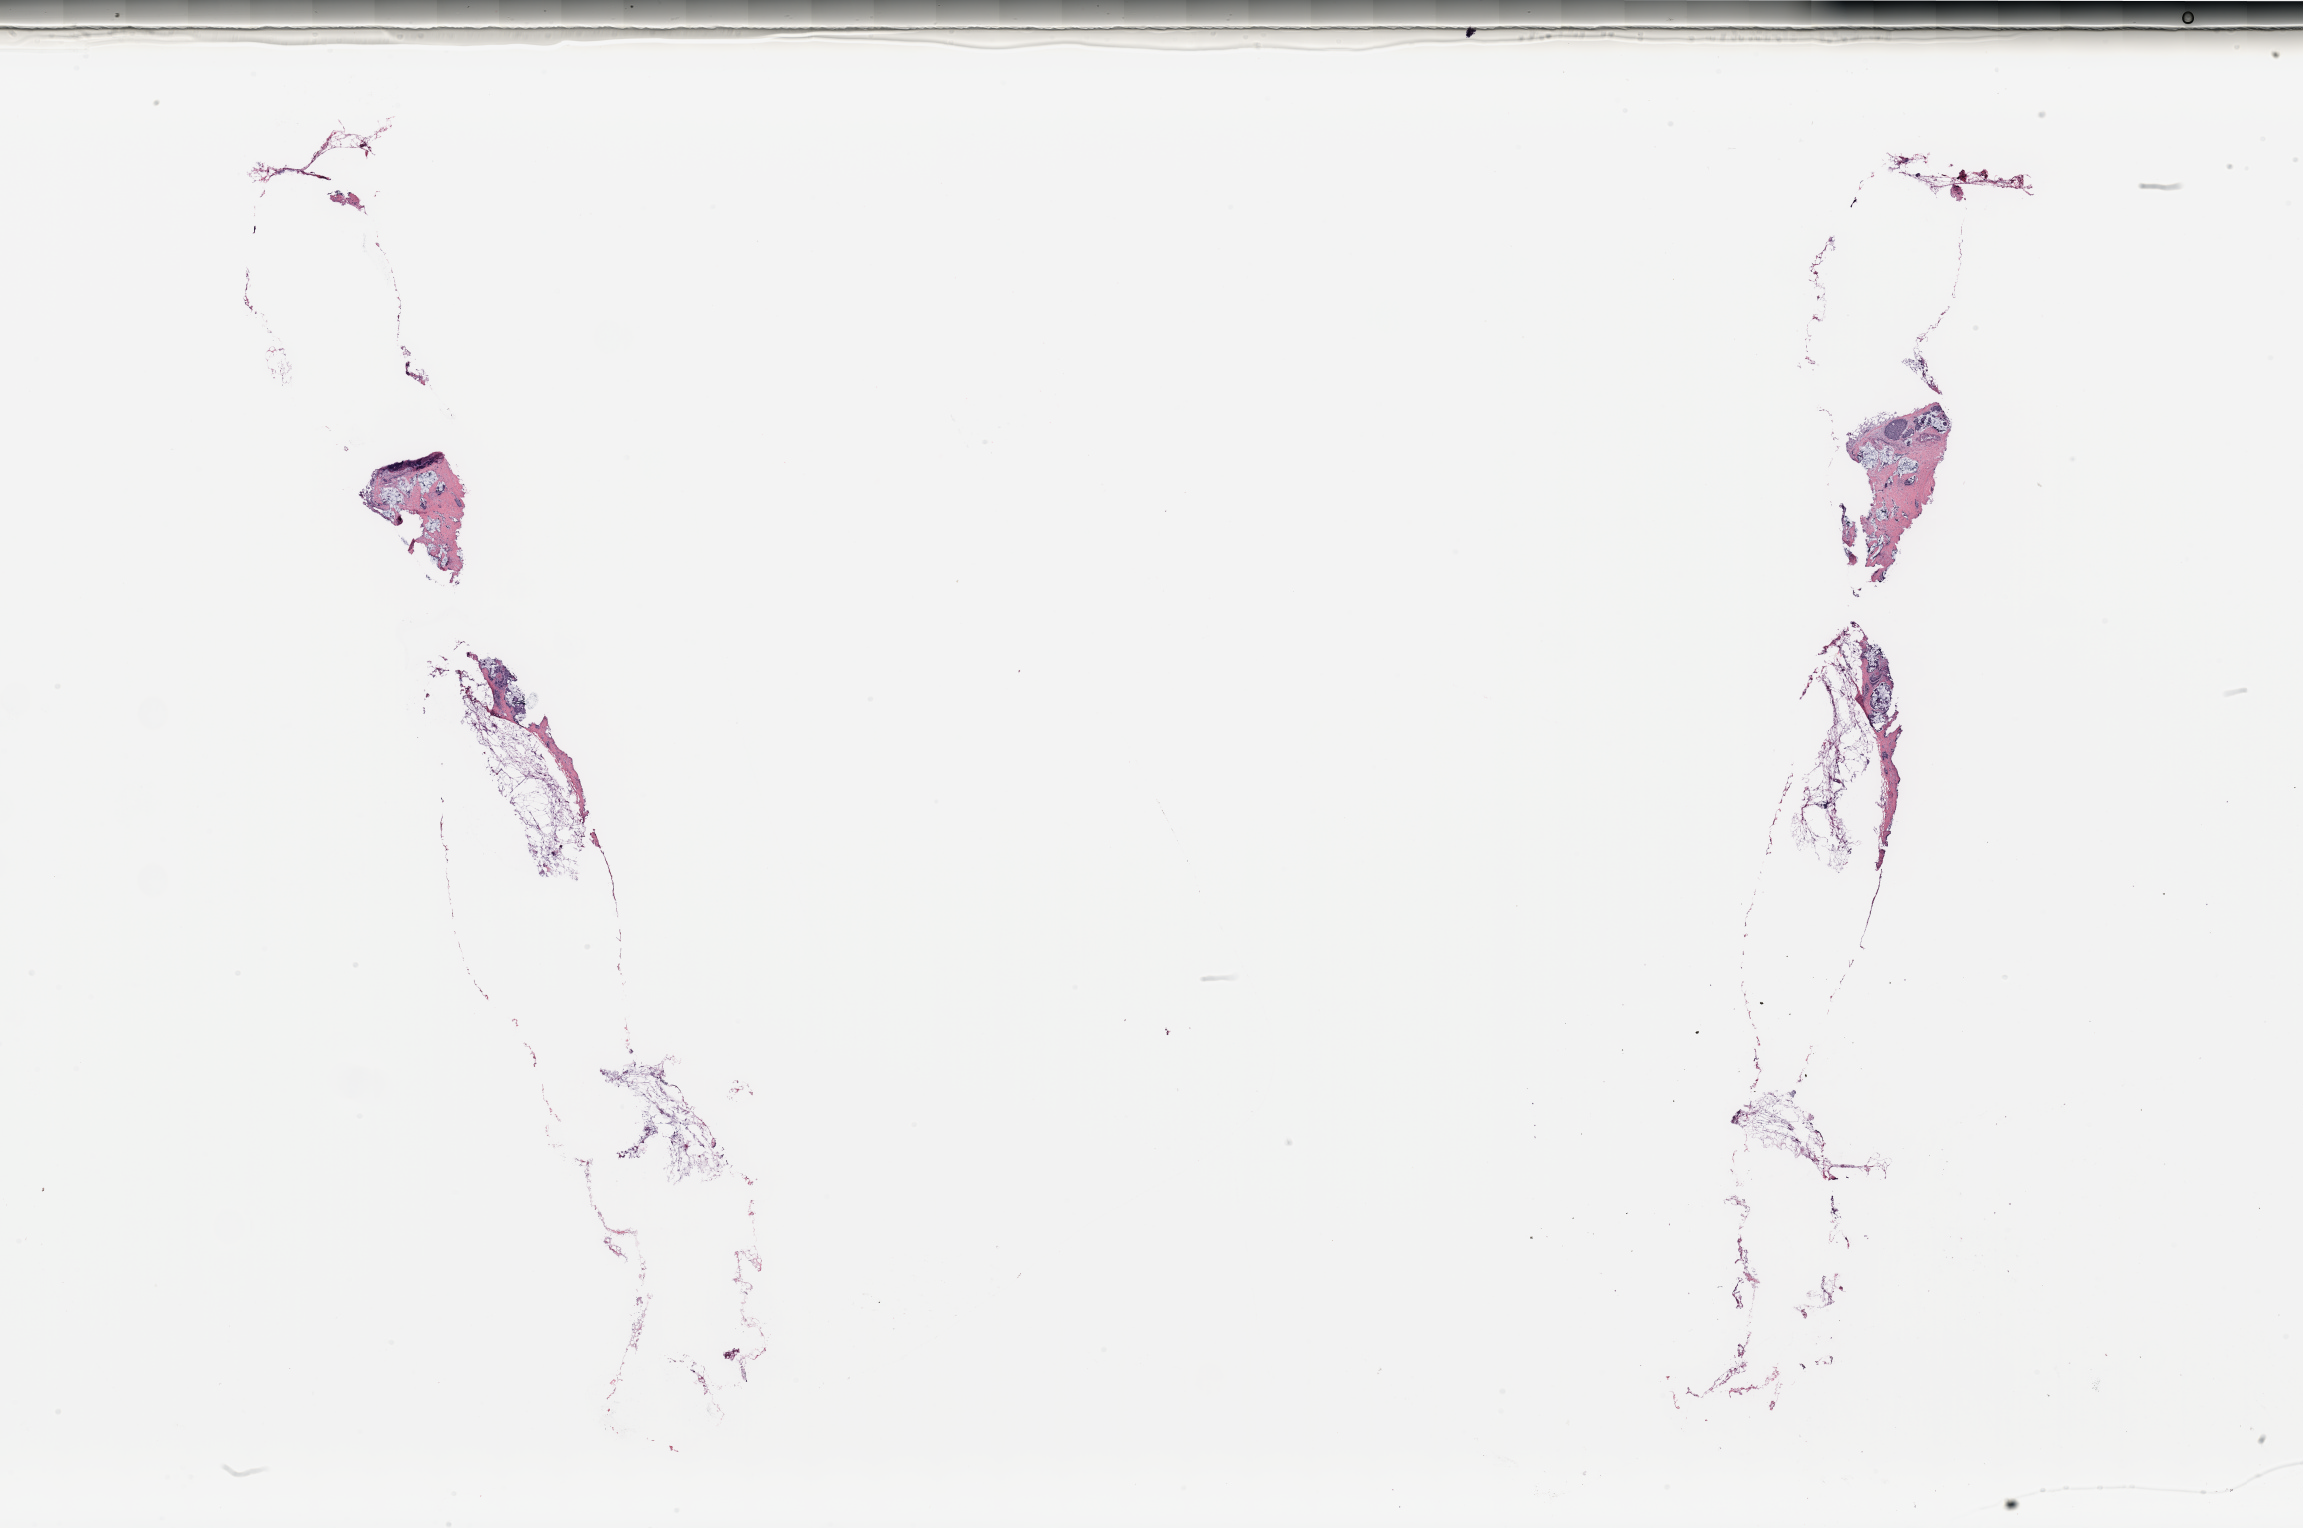
Digitized H&E-stained tissue section (whole slide), whole scanned area (about 36.4 x 24.2 mm) shown as a low-resolution overview; breast, tissue type not recorded.
Patient diagnosis (cohort enrolment): breast cancer (breast).